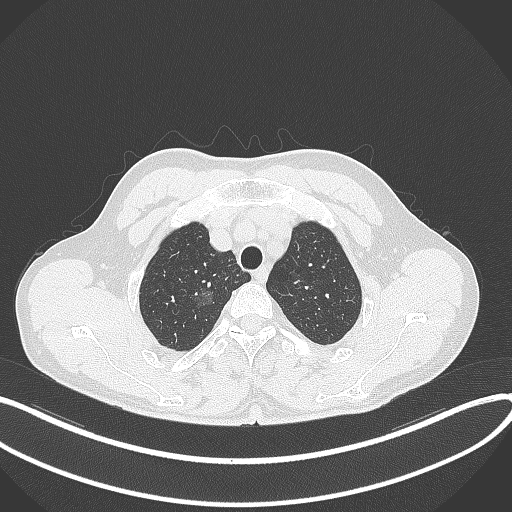
Chest CT, one axial slice. Slice 320 of 407 in the series (ordered by position). Reconstruction kernel B70f. Lung window (W 1500 / L -600 HU). 1 mm slice thickness. 512 × 512 image matrix. Male patient, age 58 years. From the clinical record (not read from this slice): clinical TNM (as recorded): T1c N0 M0.
Outlined on this slice (rectangle marked by the reading radiologist):
- lung tumour (recorded histology: adenocarcinoma): bounding box (x1, y1, x2, y2) in pixels: (182, 279, 218, 316)